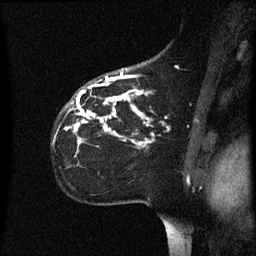
Breast MRI (dynamic contrast-enhanced), one sagittal slice; position 44 of 60 along the scan axis; dynamic contrast-enhanced series, image 2 of 3 at this slice position (ordered by acquisition); 1.5 T; TE 4.2 ms, TR 8.4 ms; 2.2 mm slice thickness; 256 × 256 image matrix, field of view 200 × 200 mm. Female patient, age 35 years. From the clinical record (not read from this slice): setting: breast cancer imaged before/during neoadjuvant chemotherapy; receptor status: HER2-positive.
Outlined on this slice (semi-automatically segmented with operator editing):
- analysis volume of interest (the breast-tissue region the enhancement analysis was run in; not a lesion): bounding box [x1, y1, x2, y2] px = [54, 78, 168, 157]
- tumour enhancement mask (voxels above the 70 % enhancement threshold inside the analysis volume of interest): [66, 78, 151, 147]